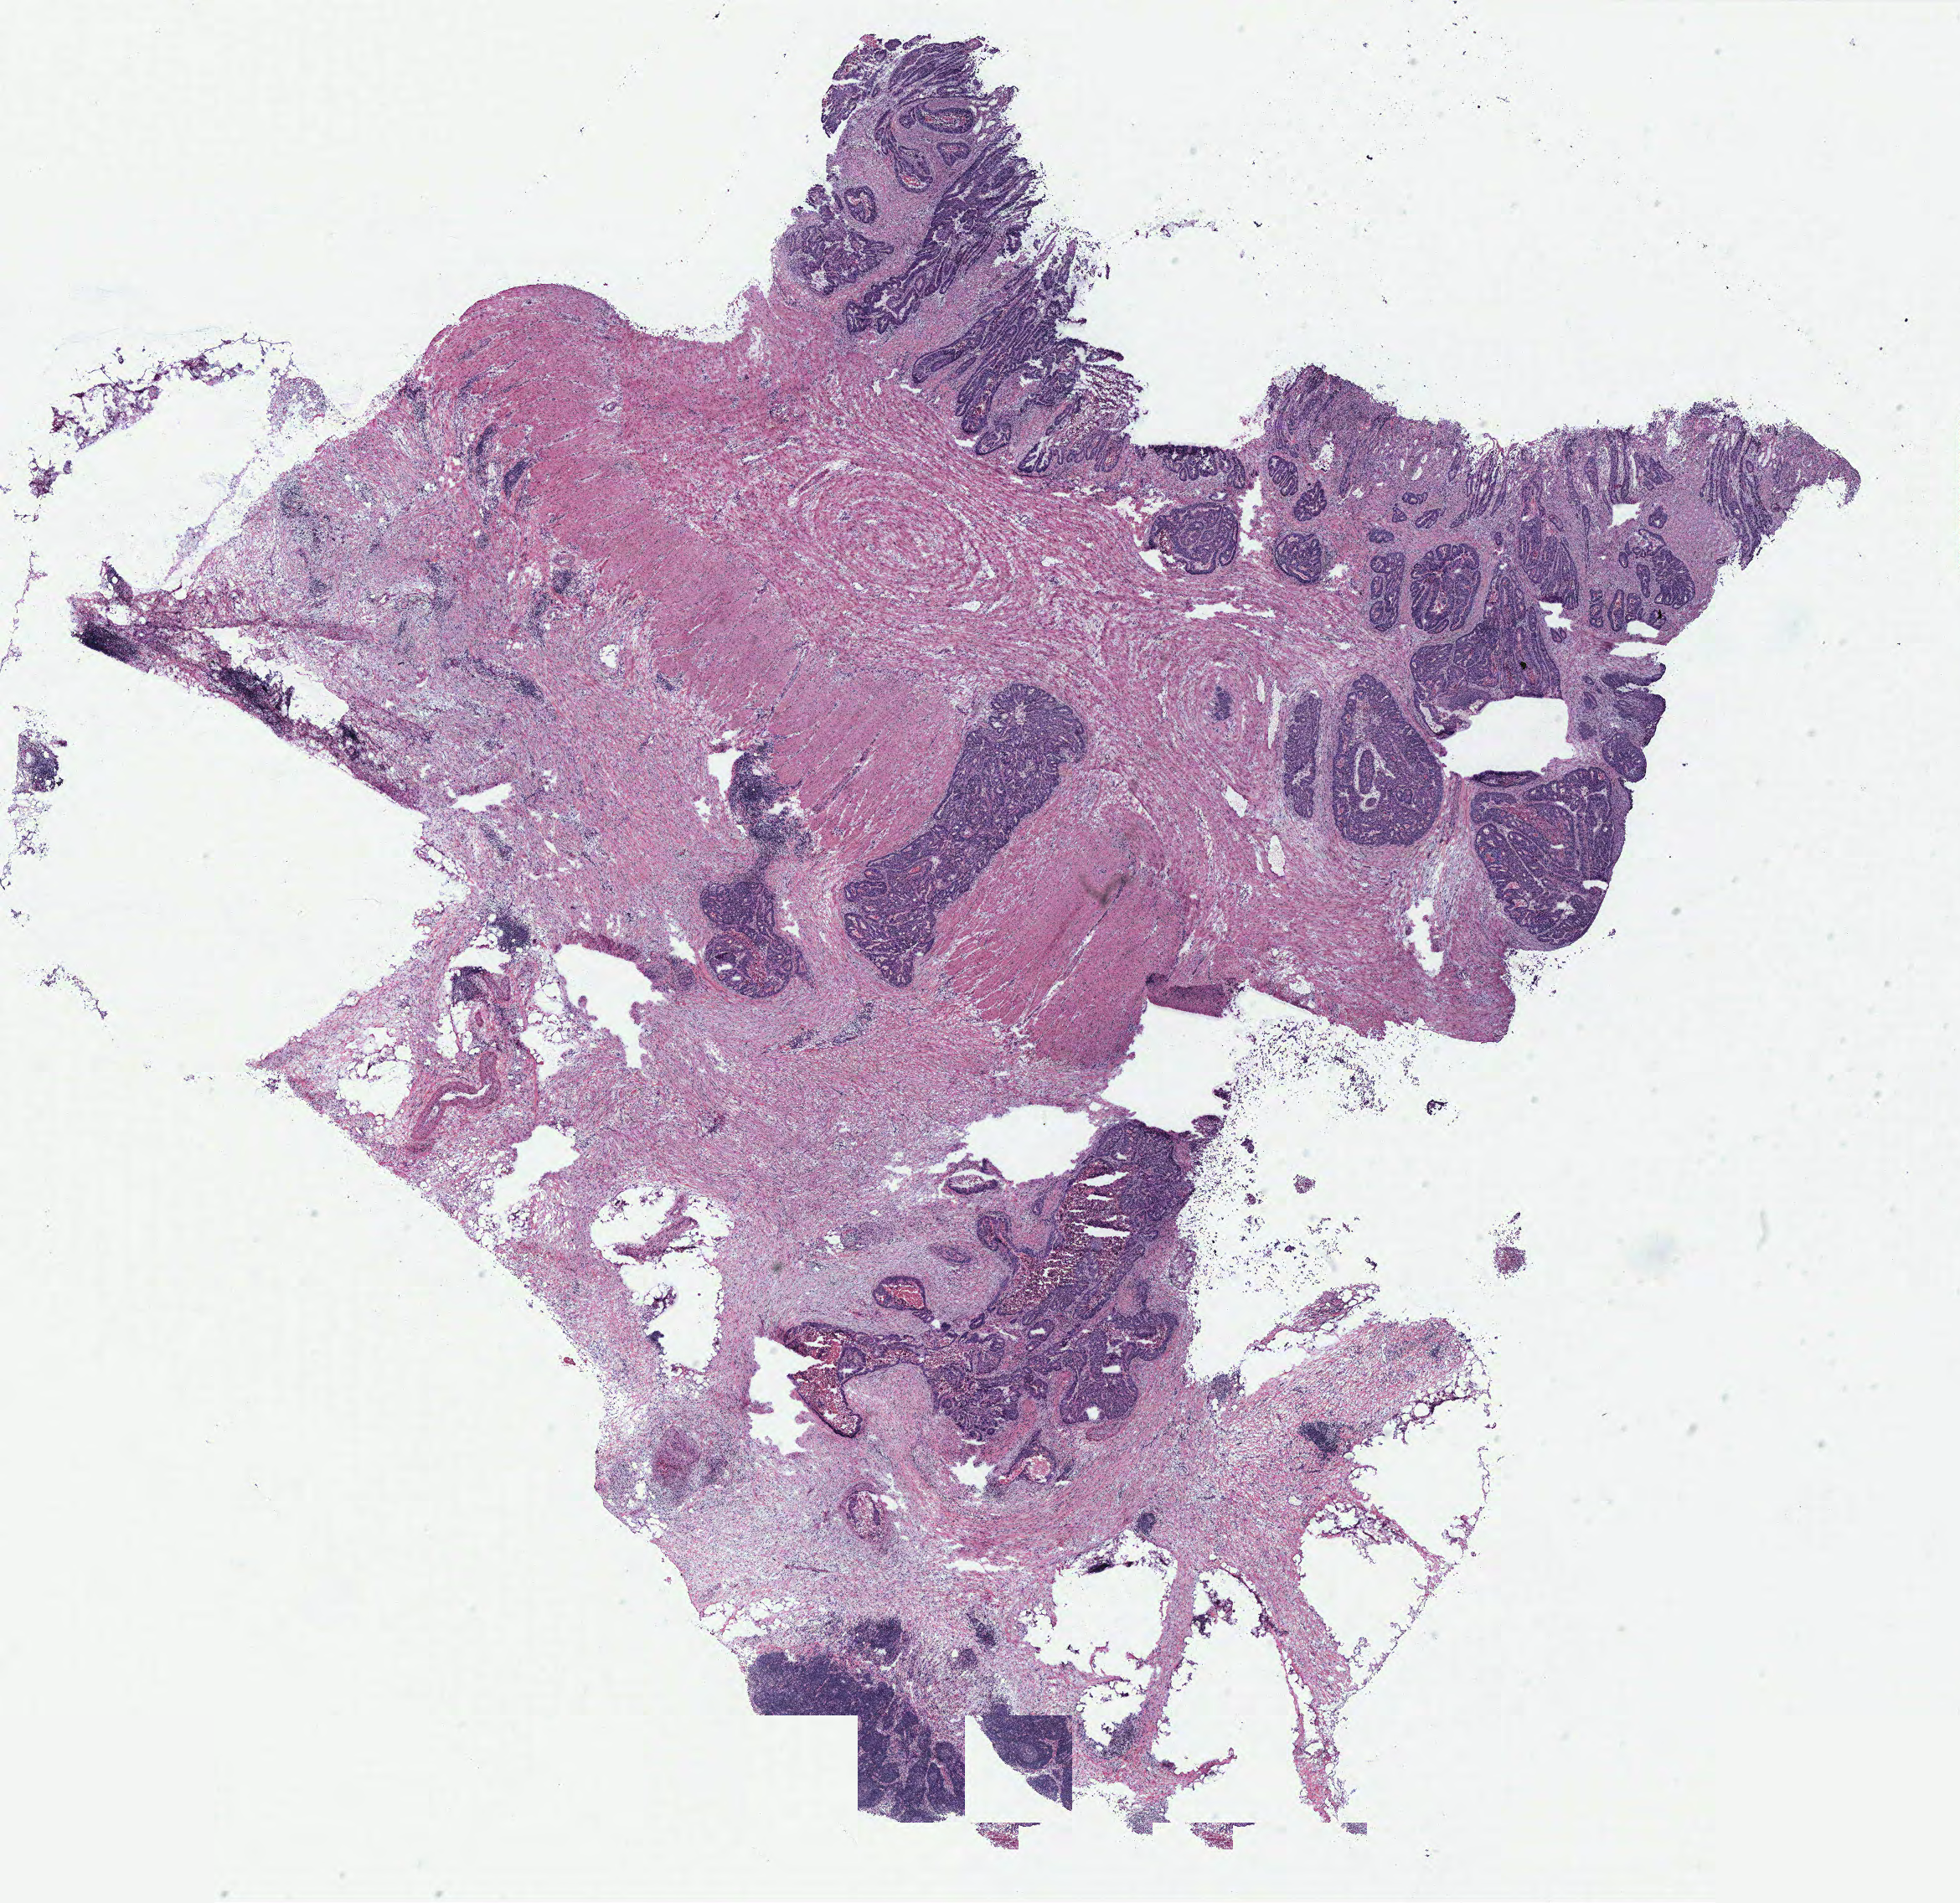
H&E whole-slide image, low-resolution overview of the scanned area, about 18.7 x 18.2 mm. Colon, tissue type not recorded.
- patient diagnosis (cohort enrolment): colon cancer (colon)